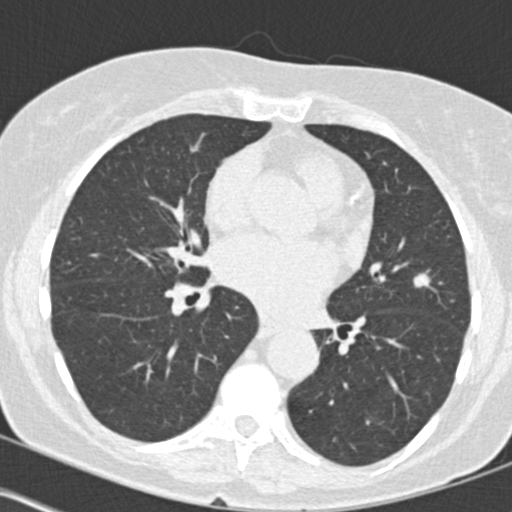
Low-dose screening chest CT, one axial slice; position 82 of 160 along the scan axis; 120 kVp; lung window (W 1500 / L -600 HU); 512 × 512 image matrix, field of view 300 × 300 mm.
Outlined on this slice (expert manual segmentation):
- lesion 1 (tumor, upper lobe of left lung): bounding box <414,274,430,287> (left, top, right, bottom; pixels)